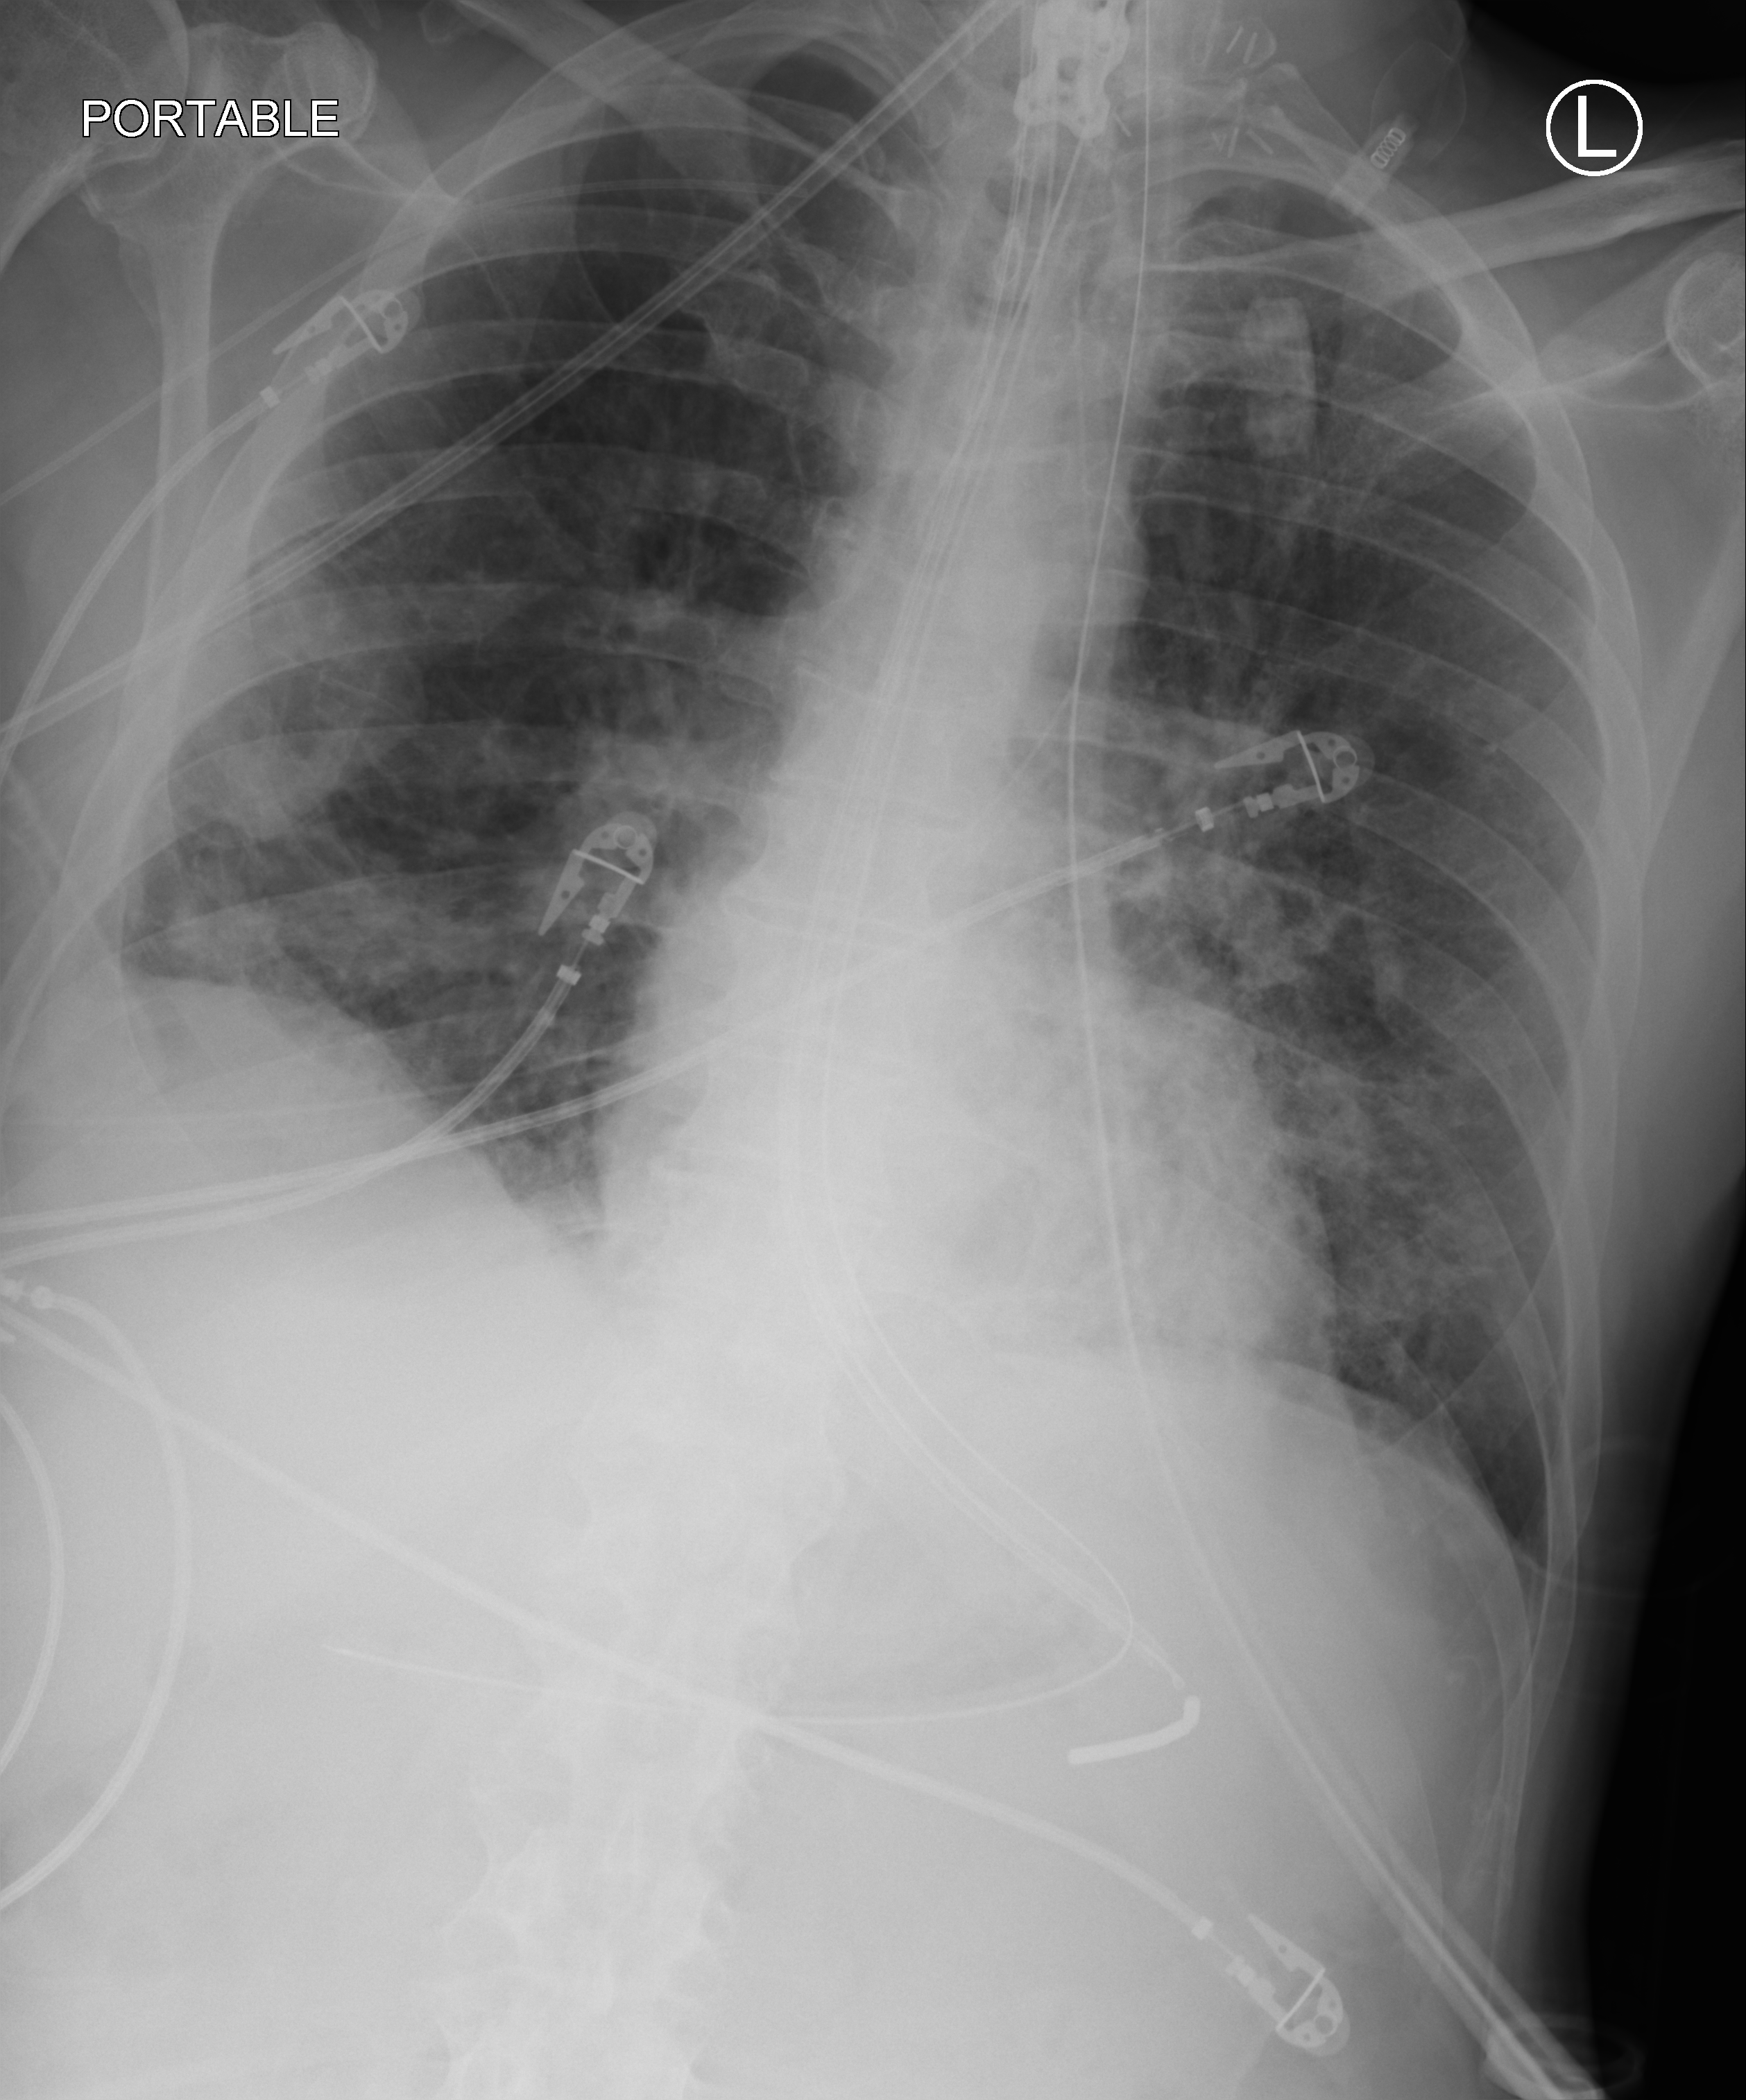
Bedside chest radiograph (computed radiography), anteroposterior (AP) projection. Male patient hospitalised with COVID-19, age 60–74 years.
Admission-level facts for this patient (not findings on this image; timing relative to this image not recorded):
- mechanically ventilated during this hospital stay: yes
- admitted to intensive care during this hospital stay: yes